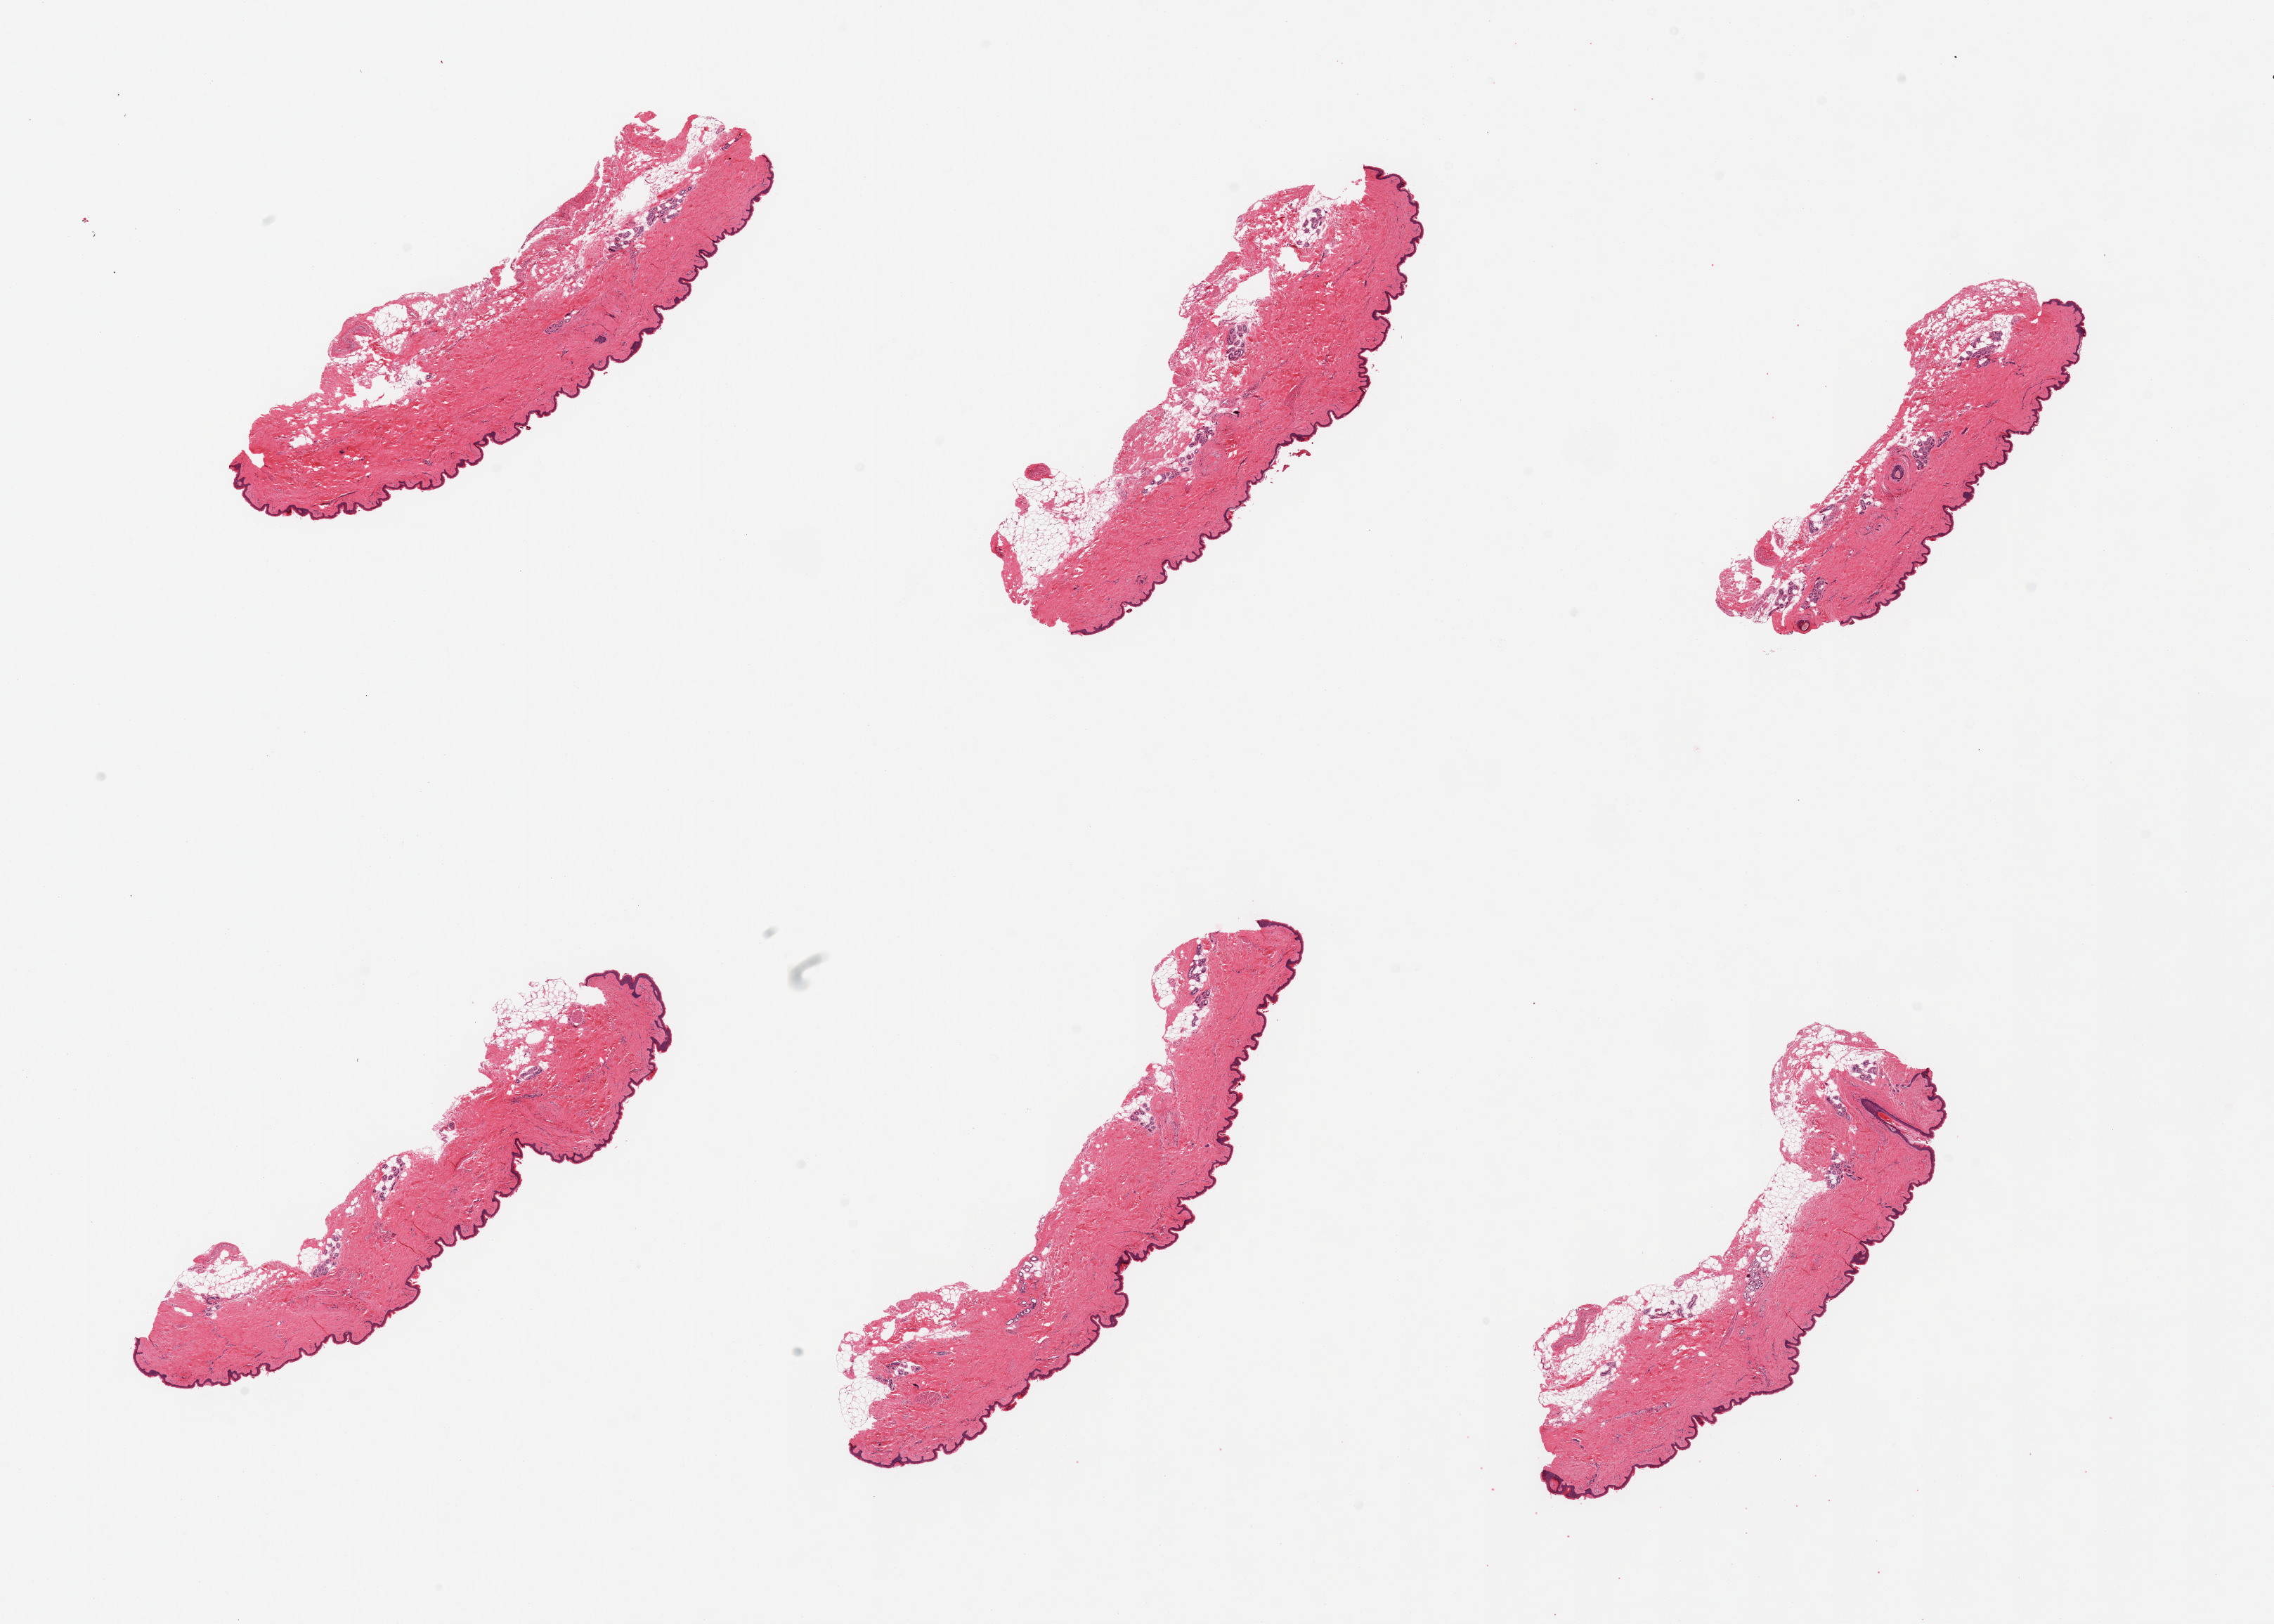
Digitized haematoxylin and eosin-stained section, whole scanned area (about 25.6 x 18.3 mm, slide scanned at 20x) shown as a low-resolution overview. PAXgene-fixed, paraffin-embedded tissue. Sampled site (target tissue): skin of suprapubic region. Tissue donor sample. Female donor.
Reviewer comment on this tissue sample: 6 pieces; 20% dermal fat.